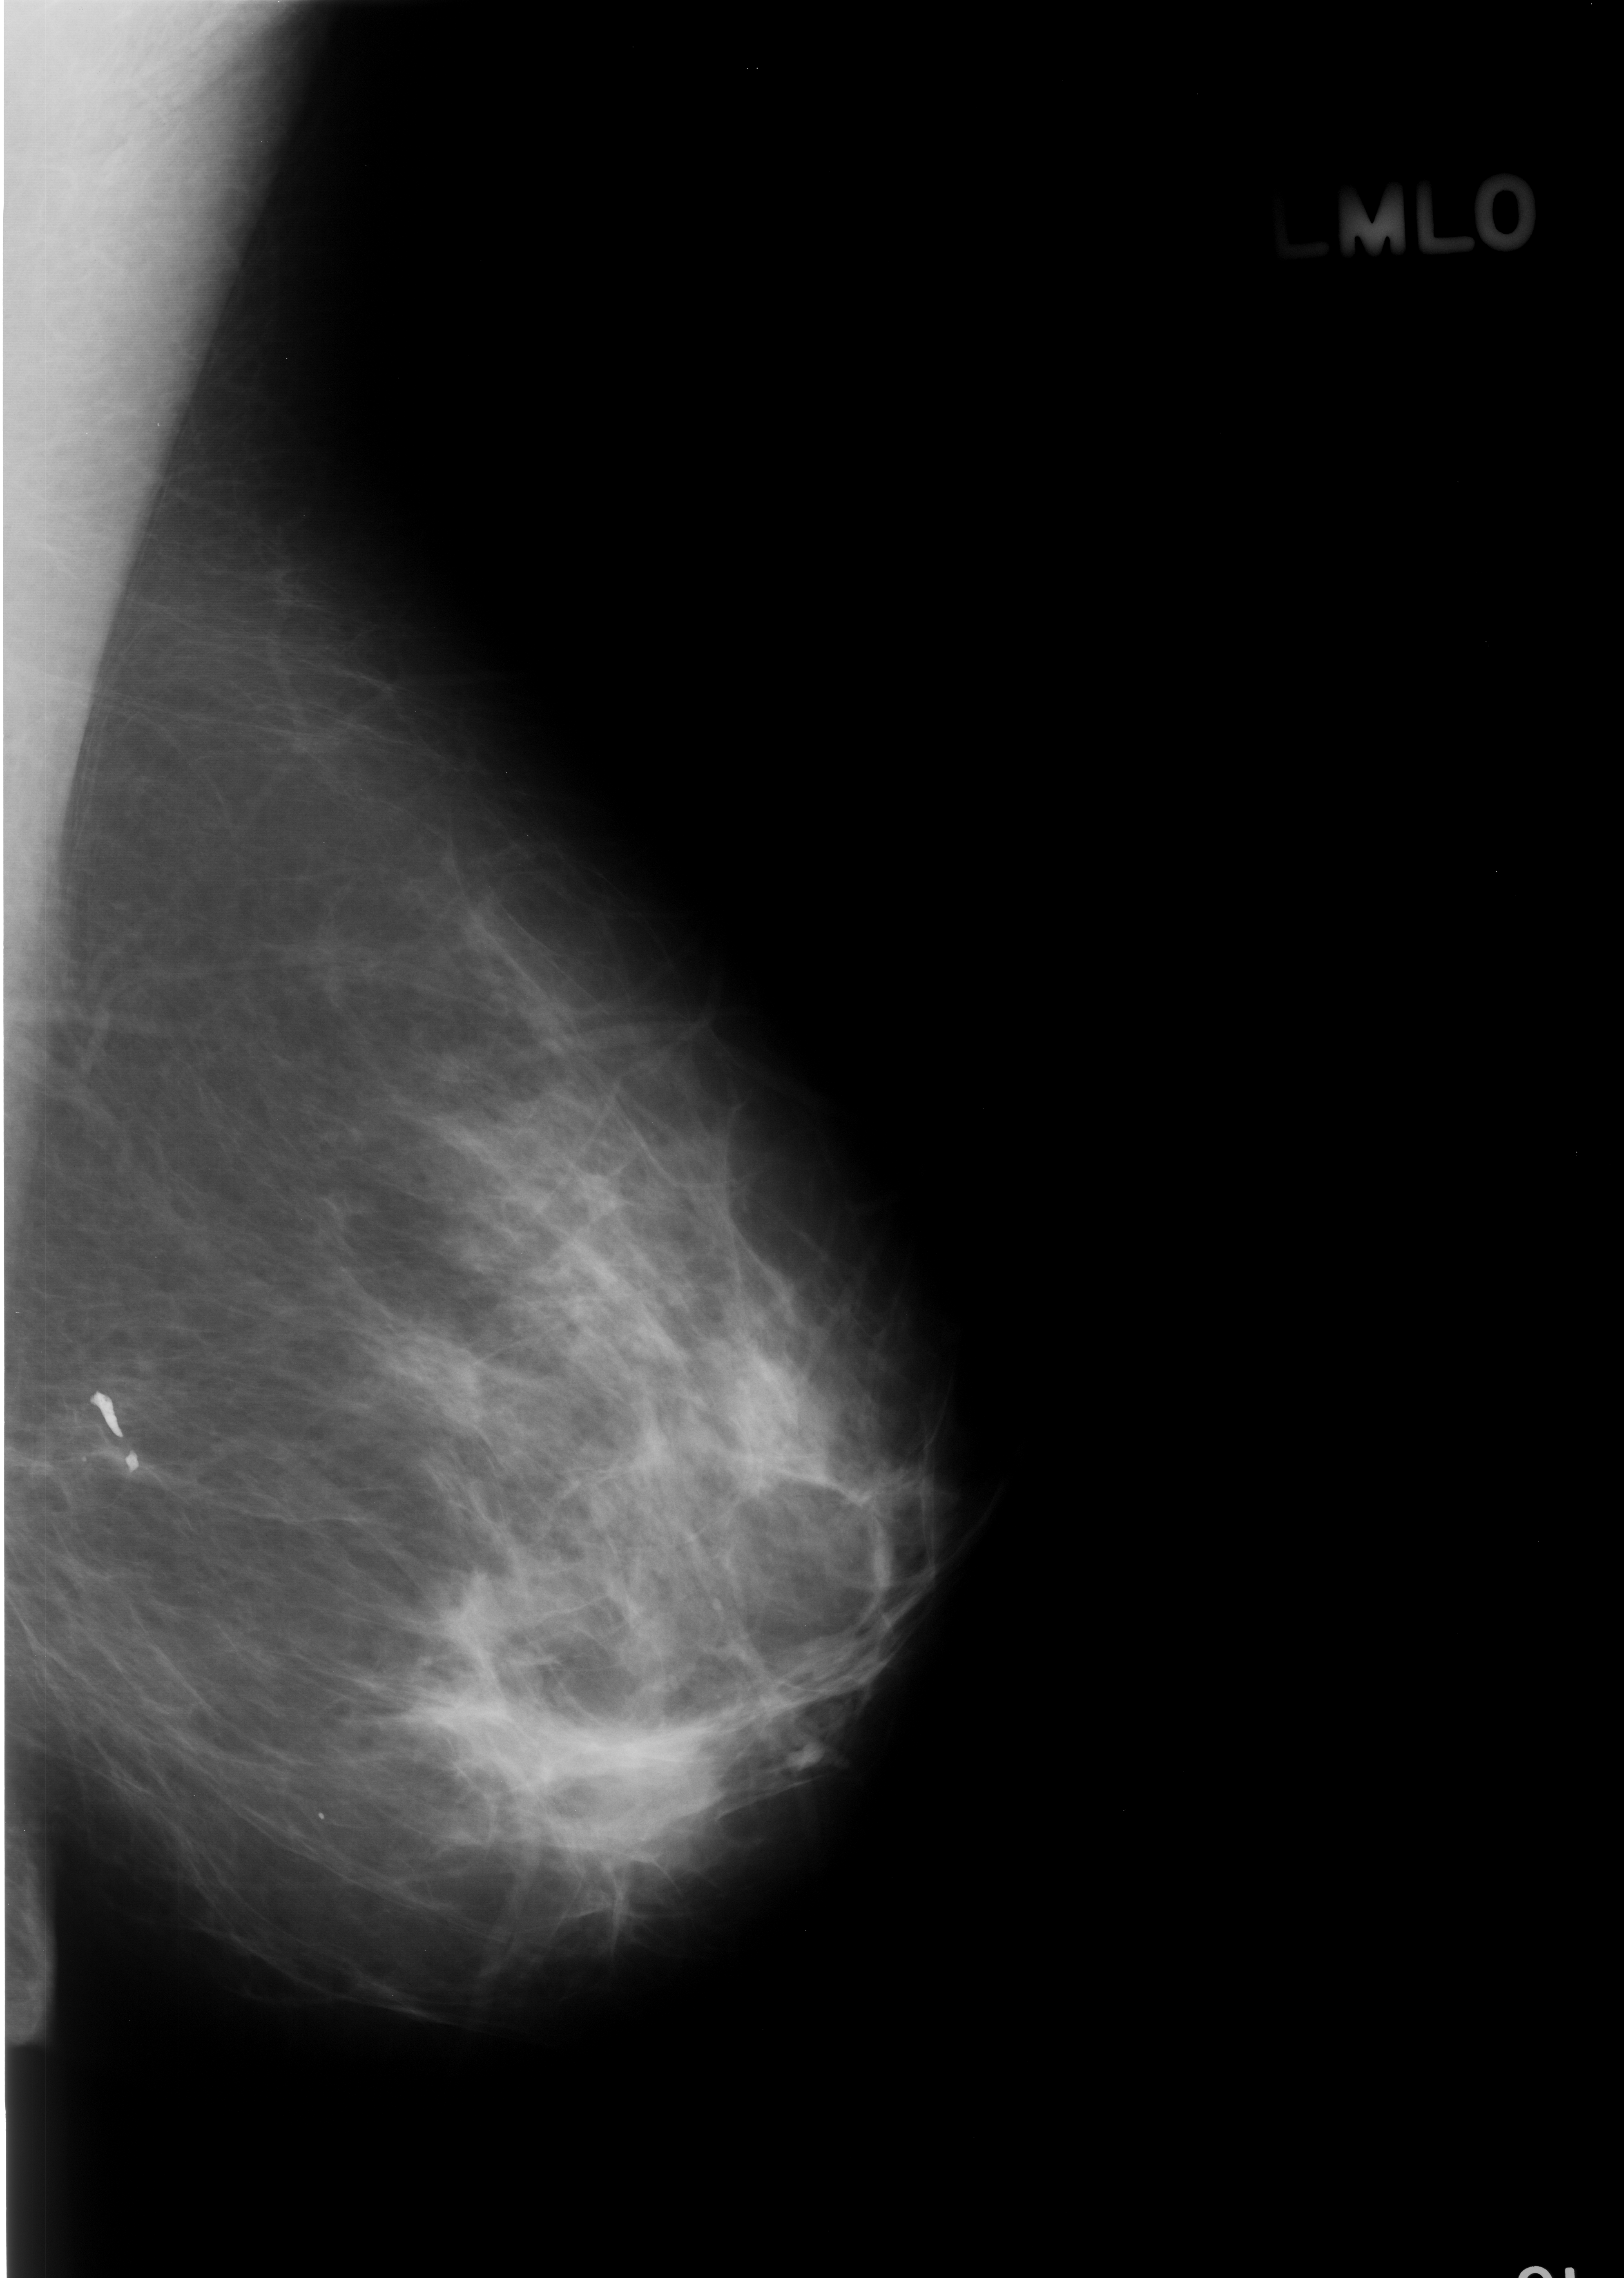
Digitized screen-film mammogram; left breast; mediolateral oblique (MLO) view; breast composition: scattered fibroglandular densities (BI-RADS density category 2 of 4).
Marked findings (only marked abnormalities are described; nothing is implied about the rest of the image): calcifications, distribution linear; BI-RADS assessment category 2; pathology result (as recorded, not read from the image): benign.